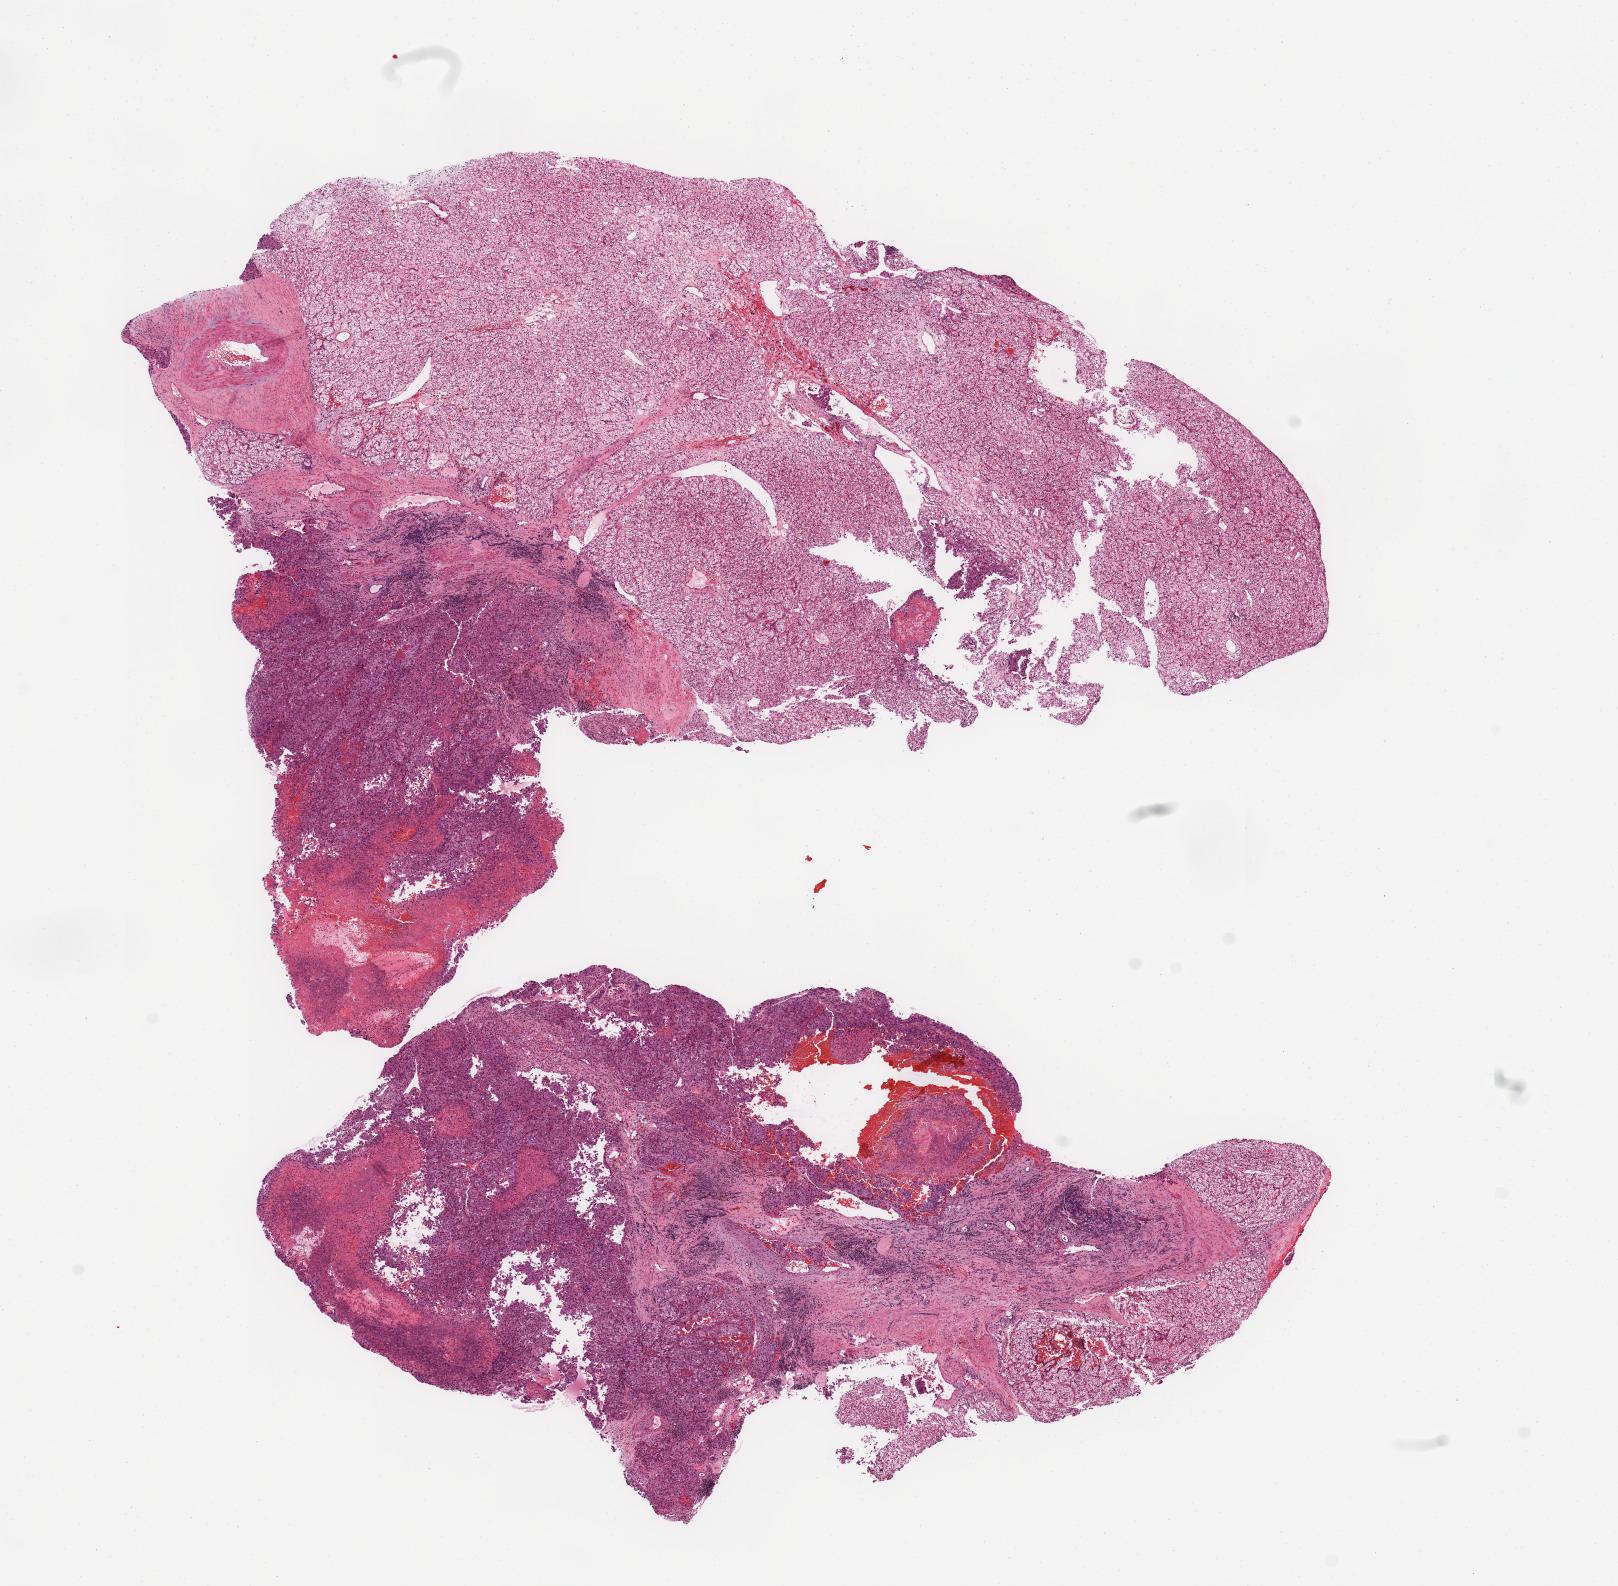
Hematoxylin and eosin (H&E) stained whole-slide image — whole scanned area (about 12.8 x 12.5 mm, slide scanned at 20x) shown as a low-resolution overview, tumour tissue sample, sampled site: kidney. Male, 60 y/o. Histologic grade: G4 (undifferentiated). Composition of this section per pathologist review: tumour nuclei 85%, necrosis 15%.
Diagnosis: Renal cell carcinoma, NOS. AJCC pathologic stage: IV.